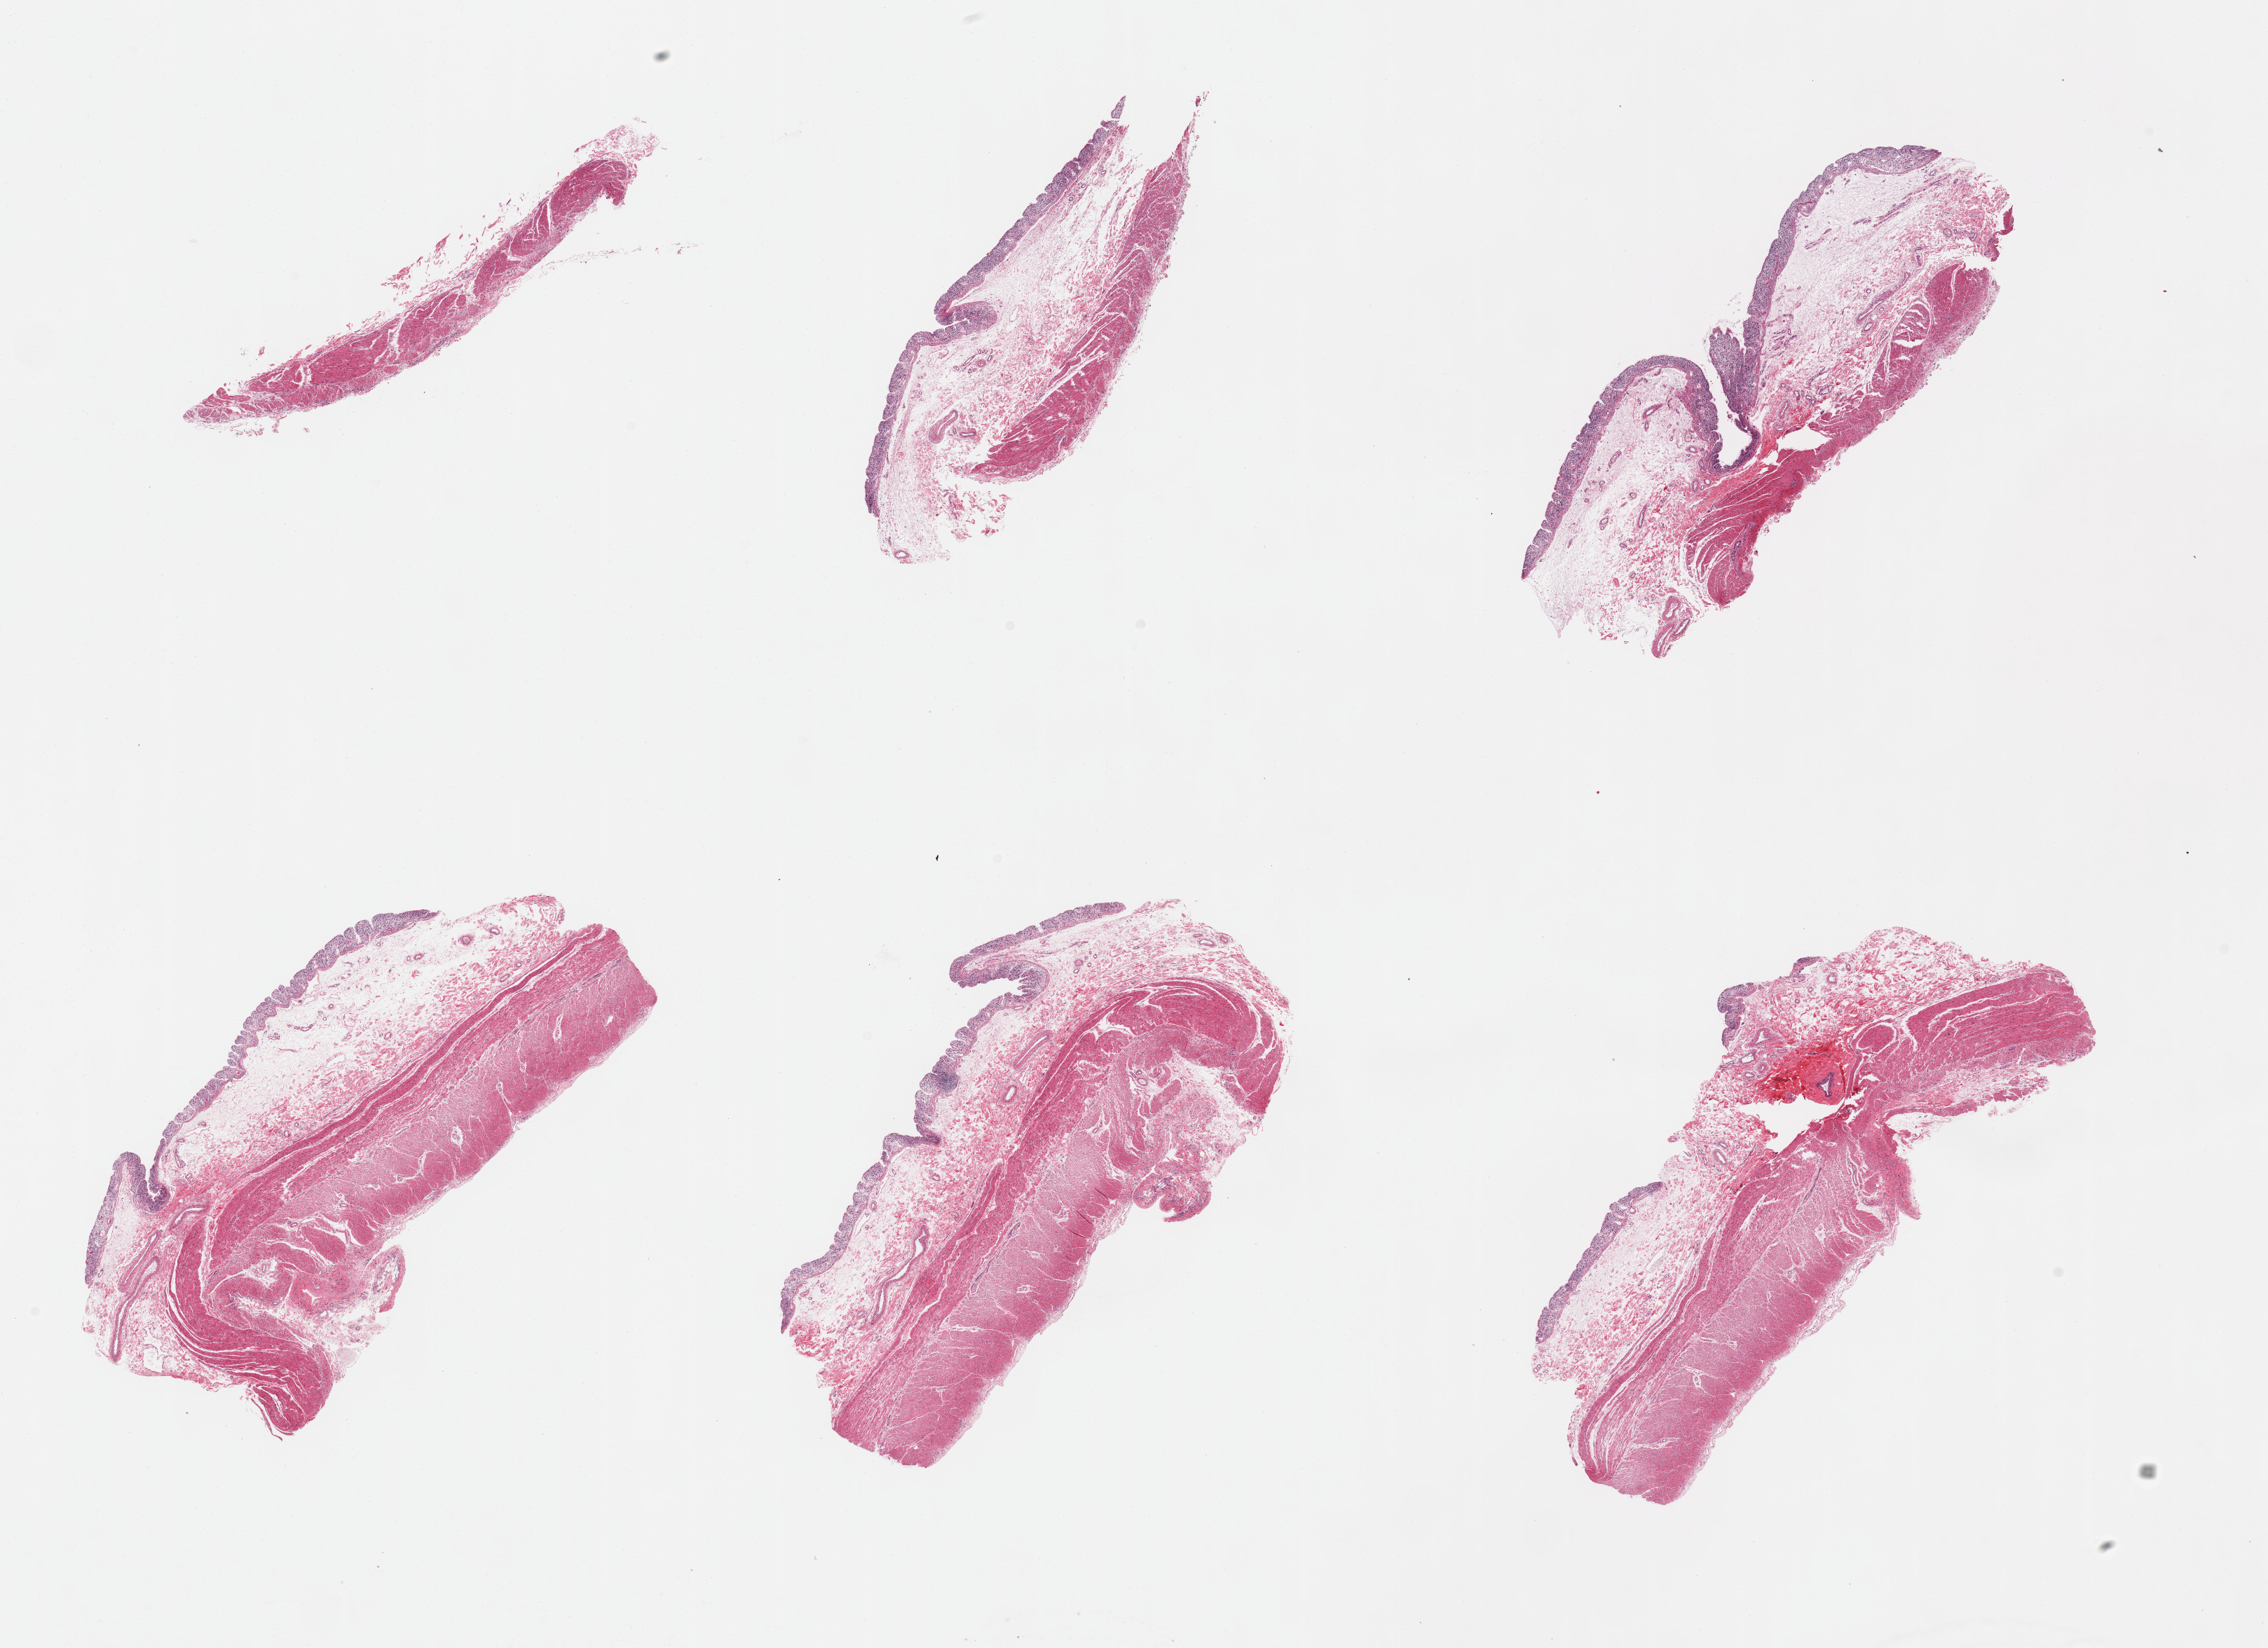
Hematoxylin and eosin (H&E) whole-slide image, a low-resolution overview of the entire scanned area, about 25.6 x 18.6 mm (acquisition: 20x scan); PAXgene-fixed, paraffin-embedded tissue; section of transverse colon (target tissue); tissue donor sample. Donor: male.
- reviewer comment on this tissue sample: 6 pieces; mucosa autolyzed; muscularis preserved